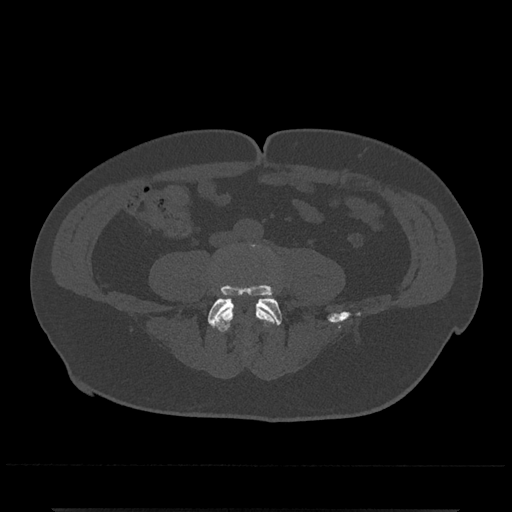
CT including the spine, one axial slice. Slice 116 of 797 in the series (ordered by position). Reconstruction kernel Br40s/3. 120 kVp. Bone window (W 1800 / L 400 HU). 0.5 mm slice thickness. 512 × 512 image matrix. Male patient, age 67 years. From the clinical record (not read from this slice): primary cancer: prostate.
Annotated regions visible in this slice (semi-automatic segmentation, software-assisted and operator-edited):
- L4 vertebra: bounding box (x1, y1, x2, y2) in pixels: (212, 302, 278, 346)
- L5 vertebra: (208, 244, 282, 326)